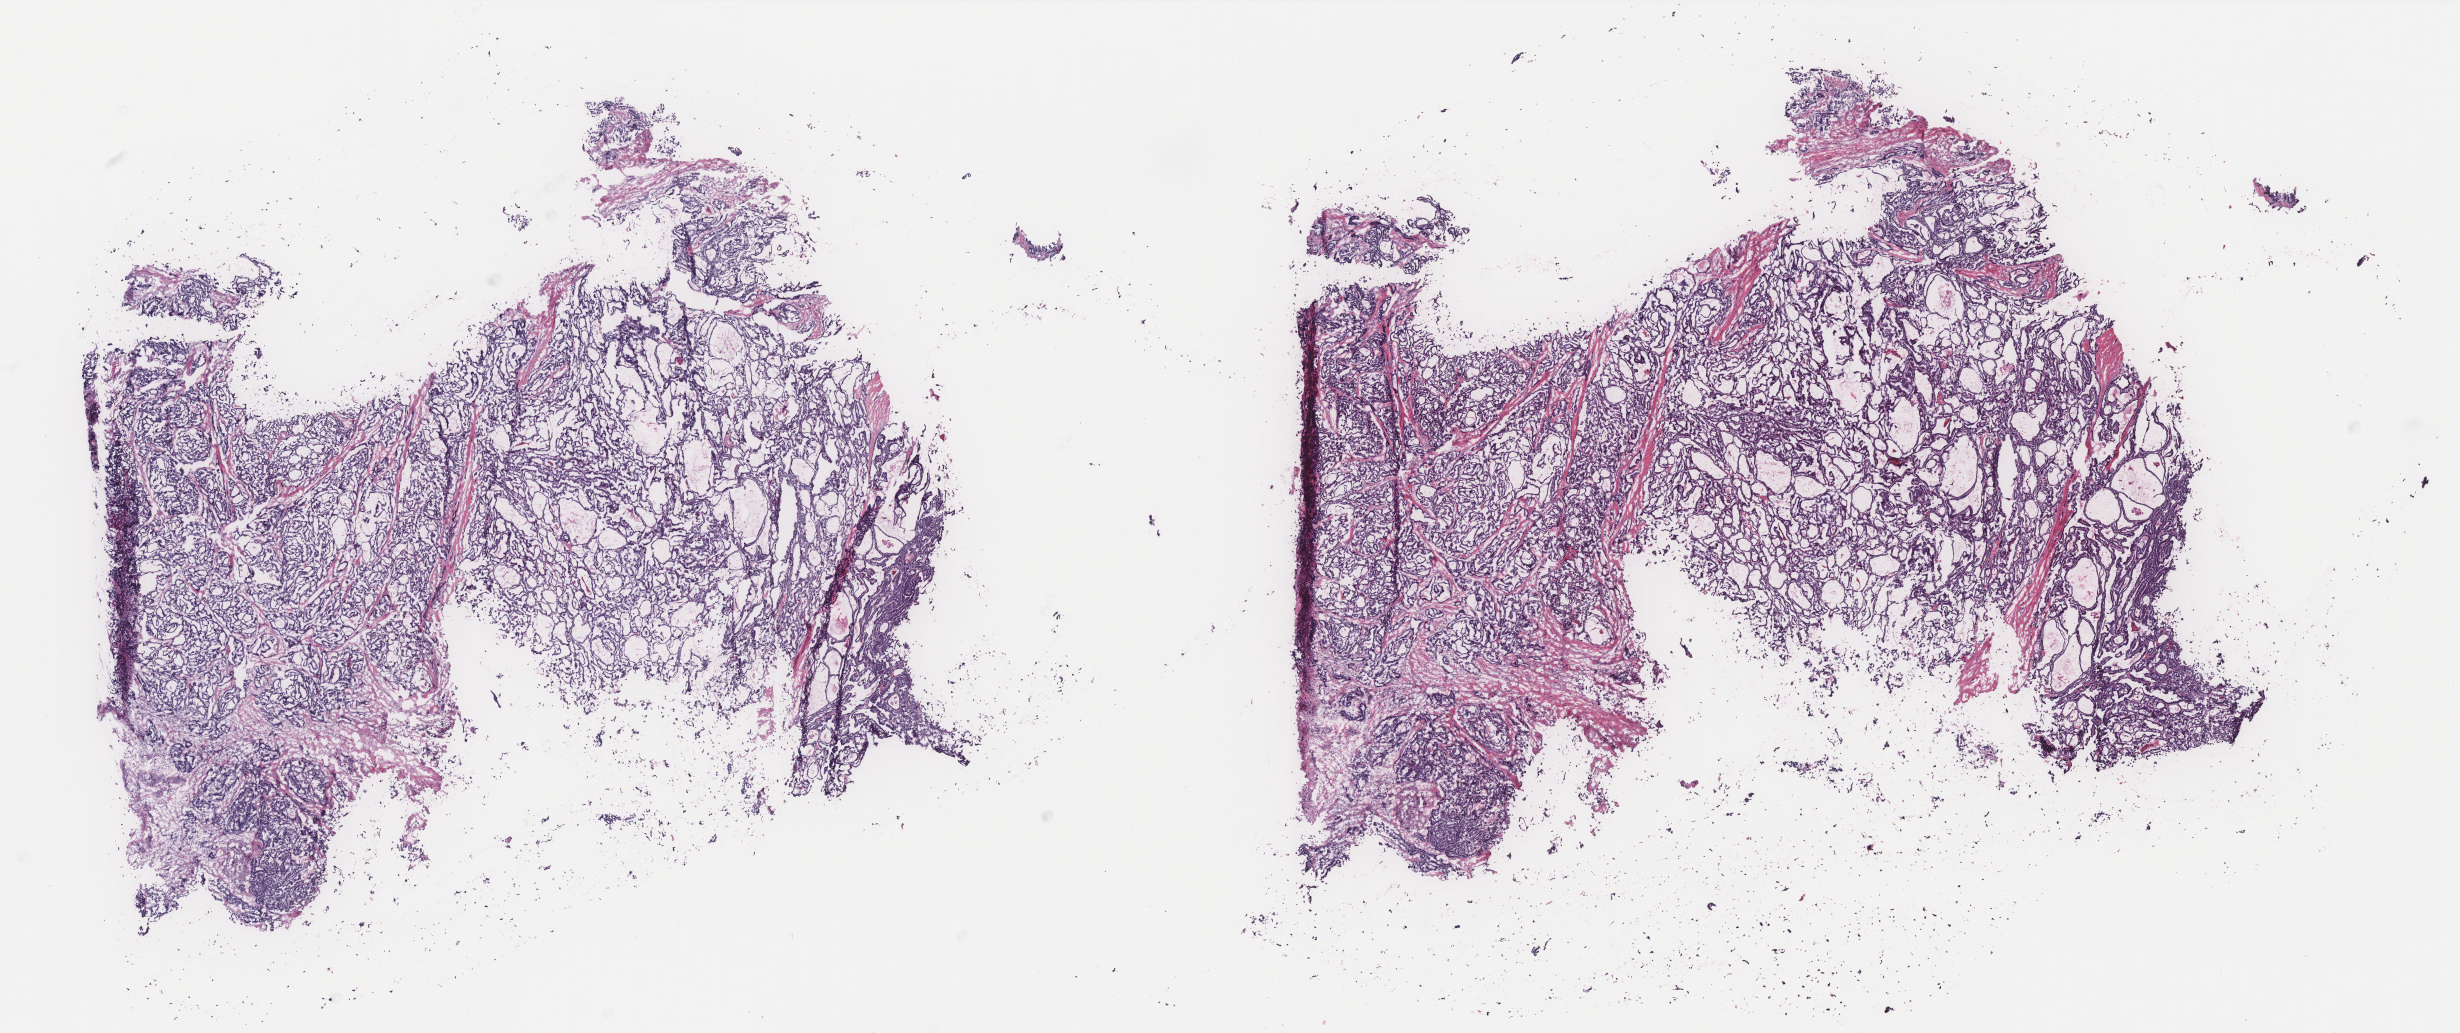
H&E-stained whole-slide image — low-resolution overview of the scanned area, about 19.7 x 8.3 mm, frozen section from the top of the tissue portion, primary tumour sample from the thyroid. Male, age 66 years at initial diagnosis. Composition of this section per pathologist review: tumour cells 85%, tumour nuclei 85%, normal cells 0%, stromal cells 15%, necrosis 0%. Inflammatory infiltration, as recorded: lymphocyte infiltration 1%, monocyte infiltration 1%, neutrophil infiltration 0%.
Diagnosis: Papillary adenocarcinoma, NOS. AJCC pathologic stage: IVA (7th edition).